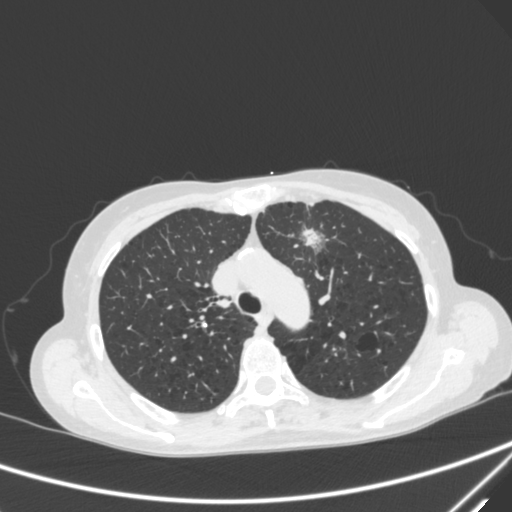
Chest CT, one axial slice; slice 223 of 300 in the series (ordered by position); 120 kVp; lung window (W 1500 / L -600 HU); 512 × 512 image matrix, field of view 350 × 350 mm. Female patient, age 71 years. From the clinical record (not read from this slice): clinical TNM (as recorded): T1c N0 M0; histopathological grade: G2-3.
Outlined on this slice (bounding box drawn by a radiologist):
- lung tumour (recorded histology: adenocarcinoma): bounding box (x1, y1, x2, y2) in pixels: (298, 219, 334, 259)